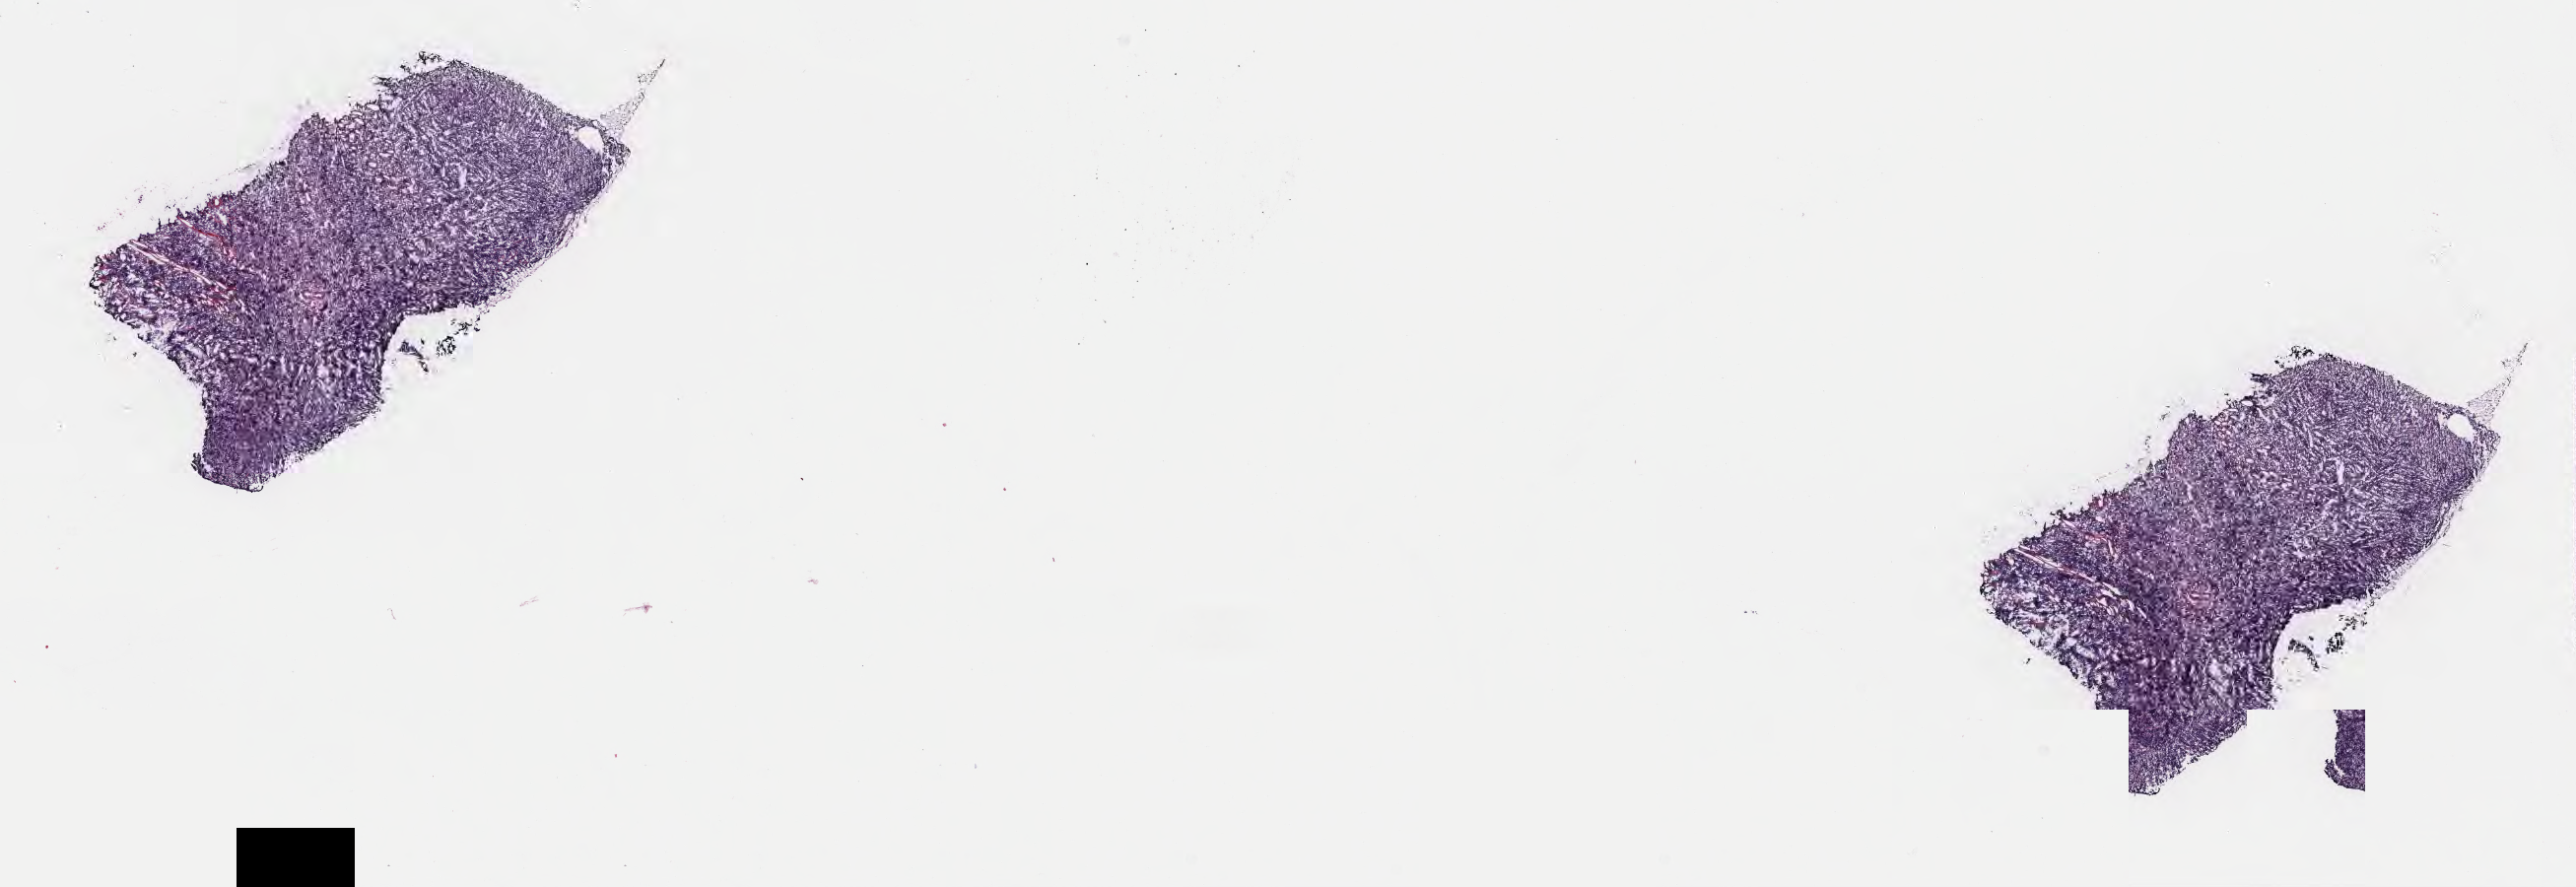
Whole-slide image, haematoxylin and eosin stain — whole scanned area (about 21.1 x 7.3 mm) shown as a low-resolution overview. Frozen section. Specimen: primary tumor. Site: mandible. Patient: male, 19 years old. Composition of this section per pathologist review: tumor cells 90%, tumor nuclei 90%, stromal cells 5%, necrosis 5%, normal cells 0%. Infiltration values recorded for this section: lymphocyte infiltration 70%, monocyte infiltration 15%, neutrophil infiltration 5%.
Histologic diagnosis: Burkitt lymphoma, NOS. Section: top of the tissue portion. Ann Arbor stage (patient): Stage III.